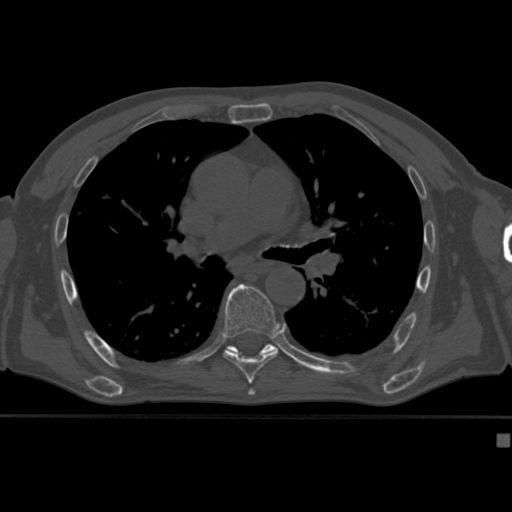
CT including the spine, one axial slice. Reconstruction kernel Br40s. Bone window (W 1800 / L 400 HU). 1.5 mm slice thickness. 512 × 512 image matrix, field of view 337 × 337 mm. Male patient, age 64 years. From the clinical record (not read from this slice): primary cancer: uterus; vertebrae with lytic lesions (as recorded): T1, T4, T5, T7, L5.
Outlined on this slice (semi-automatically segmented with operator editing):
- T7 vertebra: bounding box [x1, y1, x2, y2] px = [223, 283, 279, 382]
- T8 vertebra: [225, 344, 279, 355]